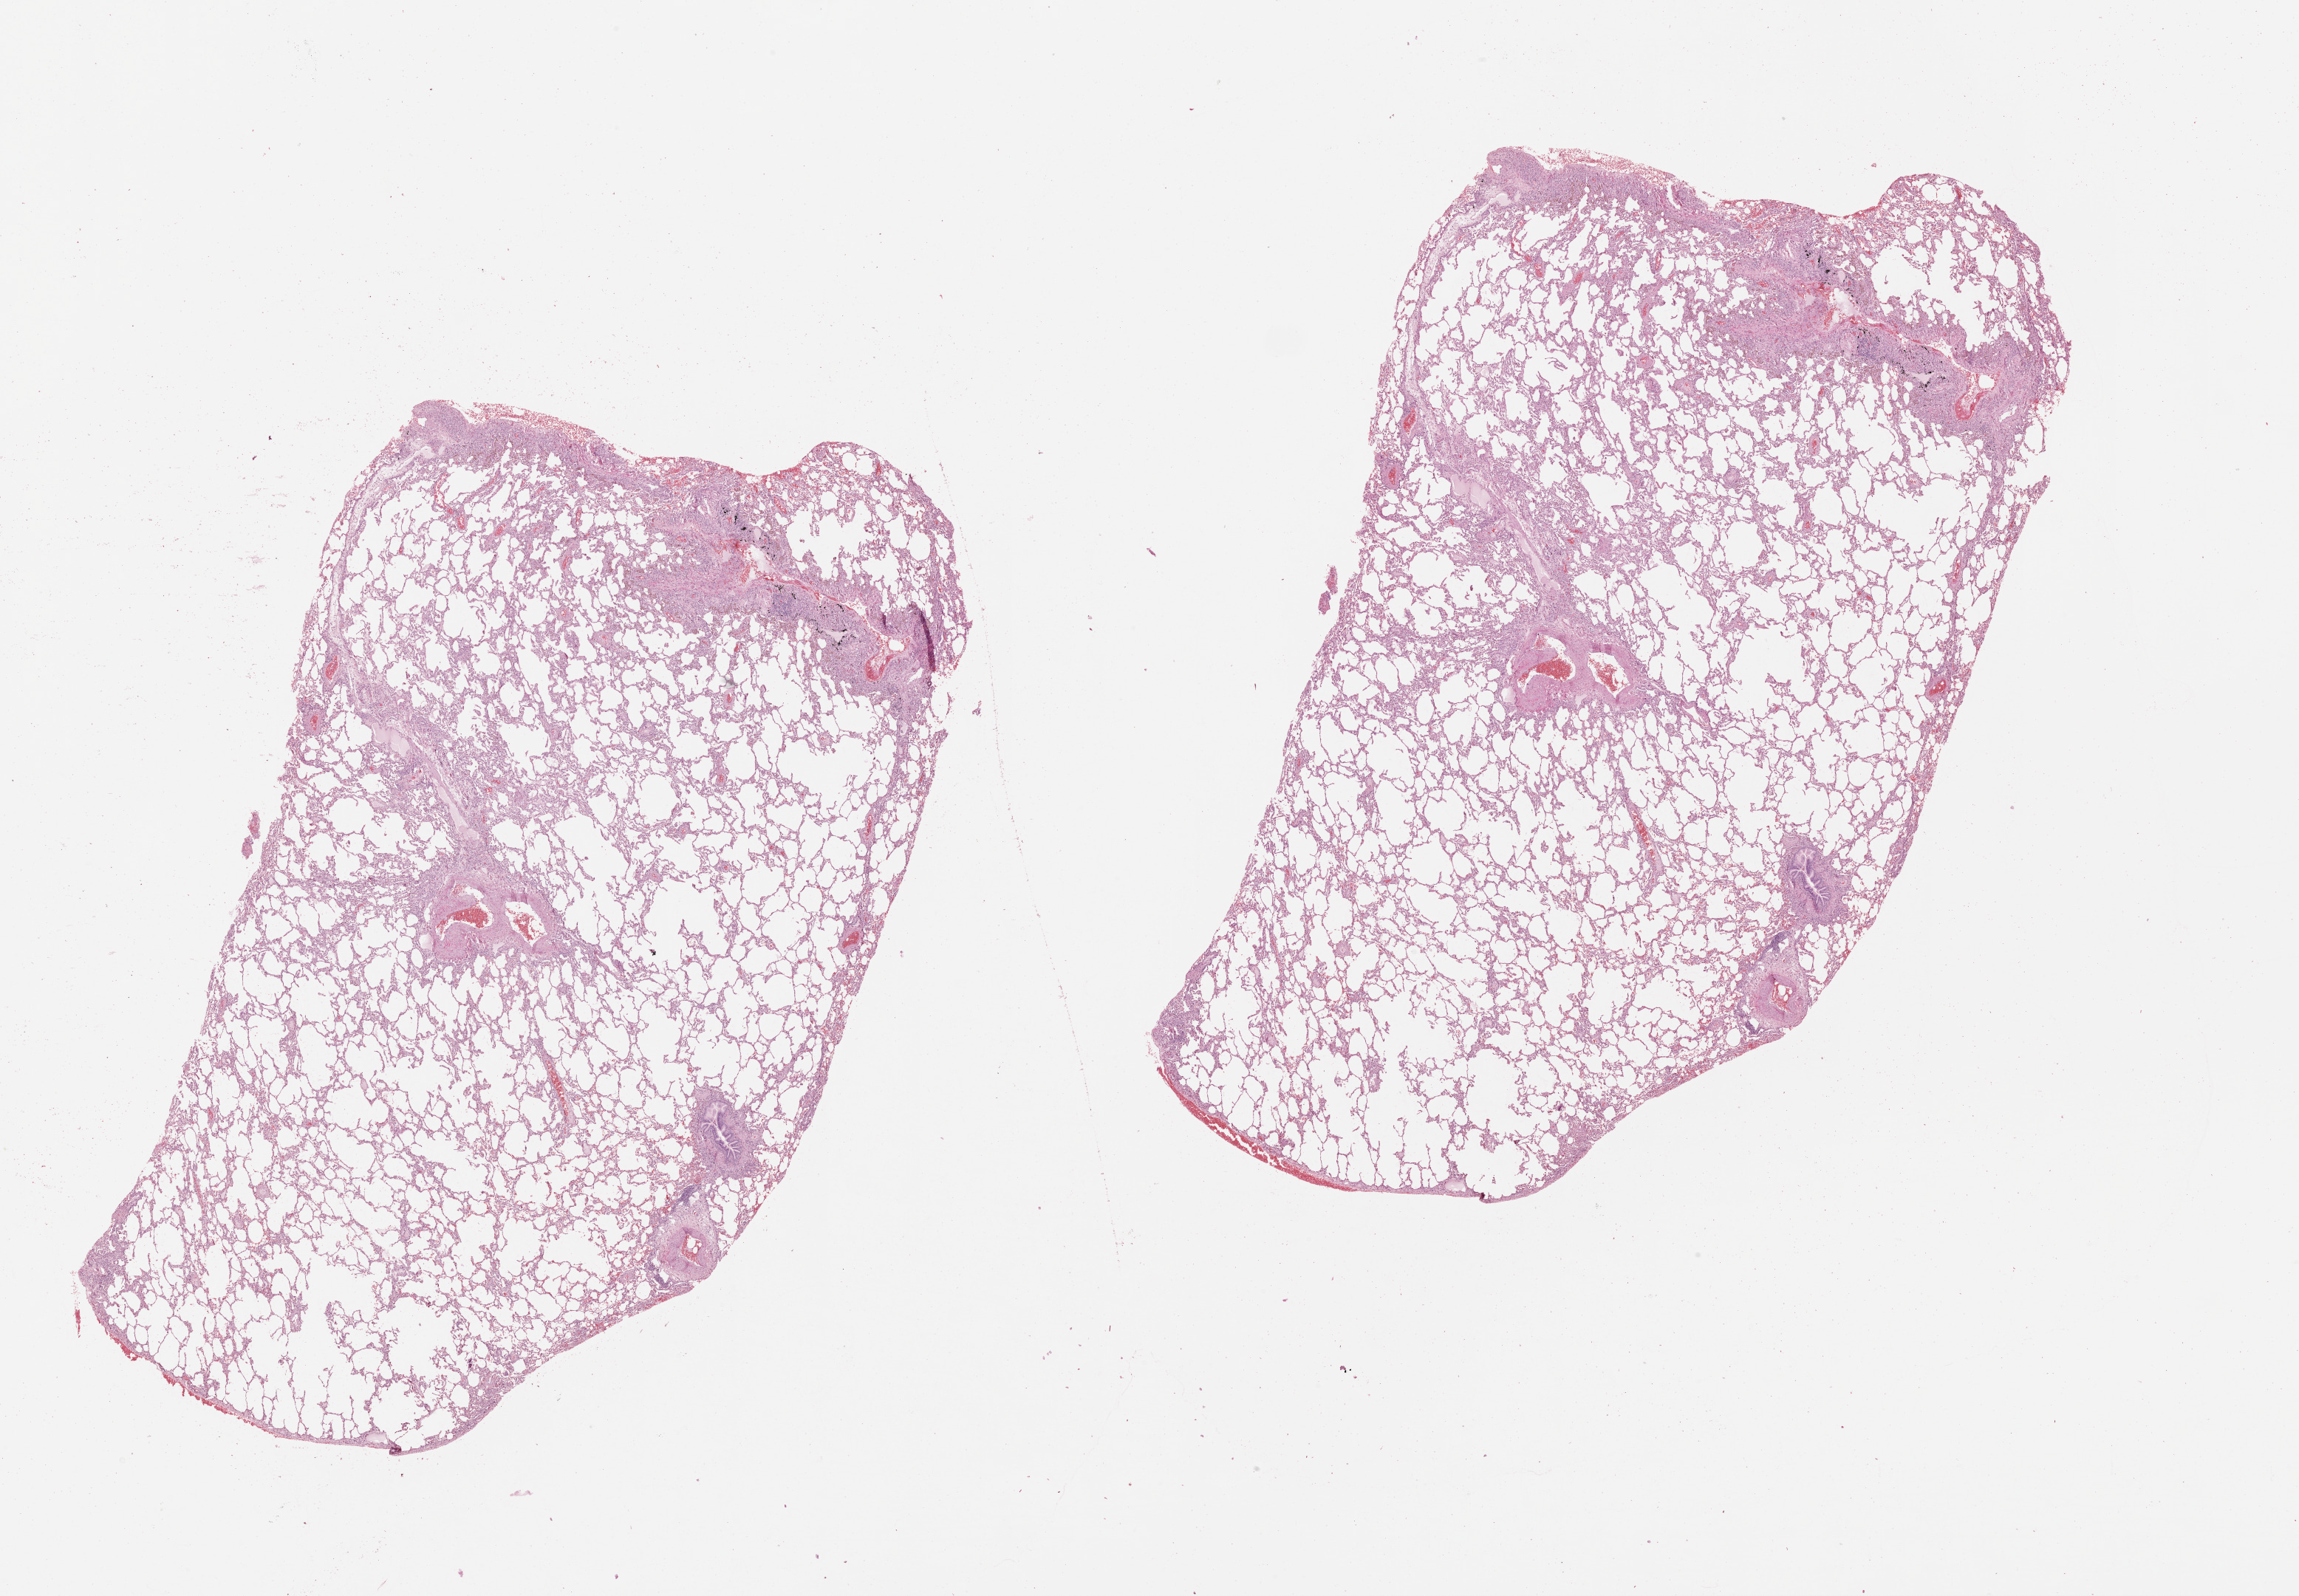
Whole-slide histology image, H&E, low-resolution overview of the scanned area, about 25.1 x 17.4 mm (from a 20x scan); lung, normal (non-tumour) tissue. Patient: male, age 56 years.
• this section: normal (non-tumour) tissue from the same patient
• patient diagnosis (cohort enrolment): squamous cell carcinoma (lung)